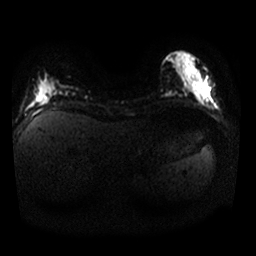
Breast MRI, one axial slice; position 8 of 25 along the scan axis; diffusion-weighted series; image 2 of 4 stored at this slice position (different b-values; order by instance number); 1.5 T; 256 × 256 image matrix, field of view 320 × 320 mm. Female patient.
Outlined on this slice (outlined manually by an expert reader):
- tumour on diffusion-weighted imaging: bounding box (x1, y1, x2, y2) in pixels: (204, 82, 209, 91)